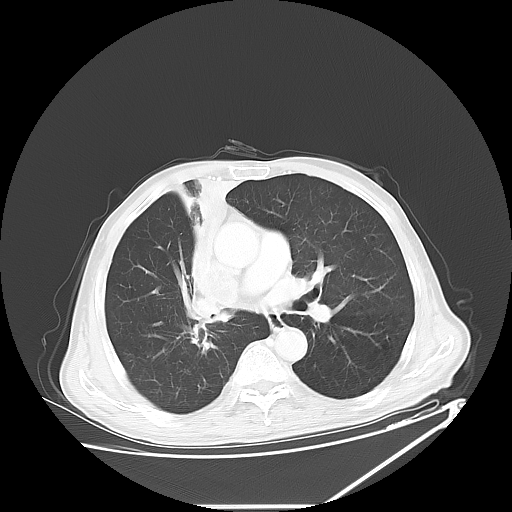
Chest CT, one axial slice. Slice 35 of 60 in the series (ordered by position). Reconstruction kernel LUNG. 120 kVp. Lung window (W 1500 / L -600 HU). 5 mm slice thickness. 512 × 512 image matrix. Male patient, age 73 years. Case-level facts recorded for this patient, not image findings: clinical TNM (as recorded): T2a N1 M0.
Outlined on this slice (bounding box drawn by a radiologist):
- lung tumour (recorded histology: squamous cell carcinoma): bounding box <175,181,236,338> (left, top, right, bottom; pixels)